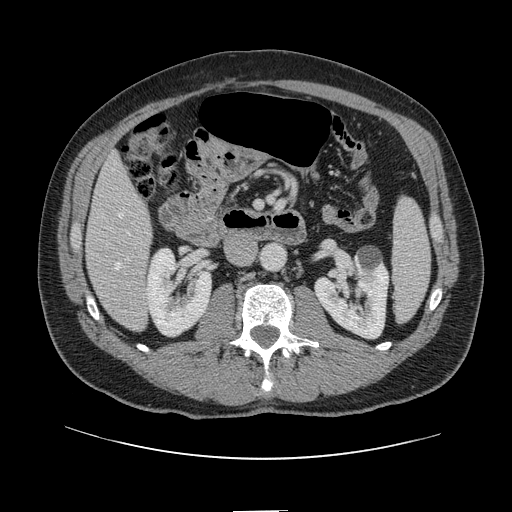
Contrast-enhanced abdominal CT, one axial slice. Position 38 of 161 along the scan axis. 120 kVp. Soft-tissue window (W 400 / L 40 HU). 2.5 mm slice thickness. 512 × 512 image matrix, field of view 412 × 412 mm. Male patient, age 66 years. Case-level facts recorded for this patient, not image findings: diagnosis: colorectal cancer liver metastases, imaged before liver resection; multiple liver metastases: no; largest metastasis: 3.5 cm; disease in both lobes: no.
Annotated regions visible in this slice (expert manual segmentation):
- hepatic veins: bounding box (x1, y1, x2, y2) in pixels: (116, 213, 123, 270)
- liver: (87, 157, 152, 330)
- planned liver remnant (the part of the liver to remain after resection): (87, 157, 149, 267)